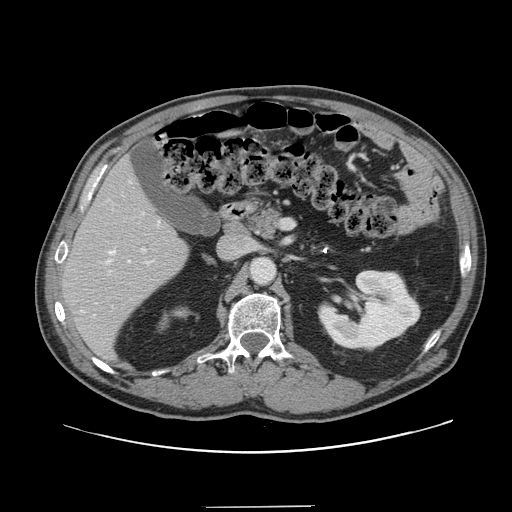
Contrast-enhanced abdominal CT, one axial slice; position 76 of 139 along the scan axis; intravenous contrast given; soft-tissue window (W 400 / L 40 HU); 2.5 mm slice thickness; 512 × 512 image matrix. Male patient, age 64 years. Case-level facts recorded for this patient, not image findings: diagnosis: colorectal cancer liver metastases, imaged before liver resection; multiple liver metastases: yes; largest metastasis: 3.5 cm; disease in both lobes: yes.
Structures marked on this image (manually delineated by an expert):
- hepatic veins: bounding box (x1, y1, x2, y2) in pixels: (94, 181, 160, 317)
- liver: (64, 161, 188, 357)
- planned liver remnant (the part of the liver to remain after resection): (63, 162, 188, 357)
- portal vein (with intrahepatic branches): (109, 248, 146, 274)